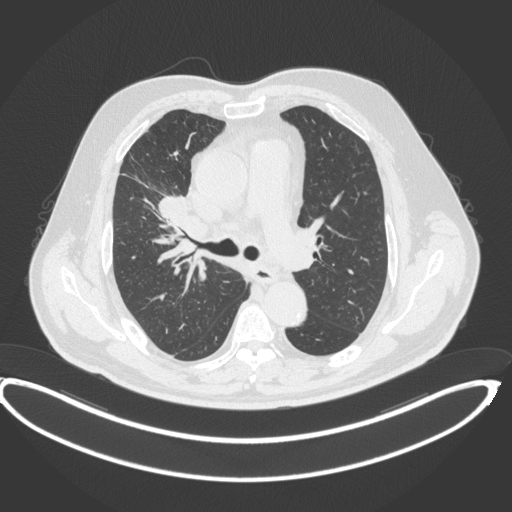
Chest CT, one axial slice; position 262 of 395 along the scan axis; reconstruction kernel B31f; lung window (W 1500 / L -600 HU); 512 × 512 image matrix, field of view 448 × 448 mm. Patient: male, 62 years. Case-level facts recorded for this patient, not image findings: clinical TNM (as recorded): T1c N3 M1c.
Outlined on this slice (rectangle marked by the reading radiologist):
- lung tumour (recorded histology: adenocarcinoma): bounding box <155,189,193,223> (left, top, right, bottom; pixels)